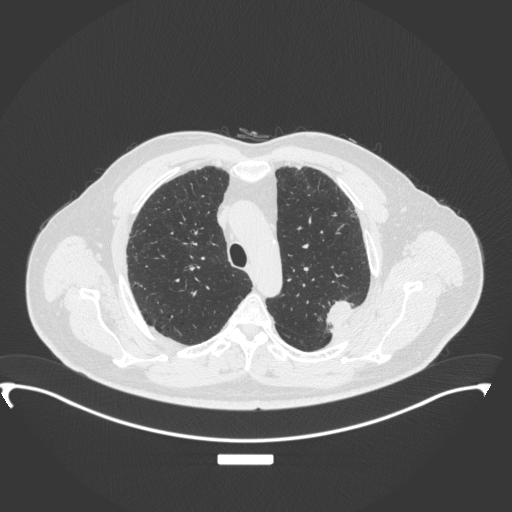
Chest CT, one axial slice. Position 272 of 350 along the scan axis. Reconstruction kernel B31f. 120 kVp. Lung window (W 1500 / L -600 HU). 1 mm slice thickness. 512 × 512 image matrix, field of view 459 × 459 mm. Patient: male, 64 years. Case-level facts recorded for this patient, not image findings: clinical TNM (as recorded): T1c N1 M1.
Annotated regions visible in this slice (rectangle marked by the reading radiologist):
- lung tumour (recorded histology: adenocarcinoma): bounding box (x1, y1, x2, y2) in pixels: (318, 294, 356, 331)